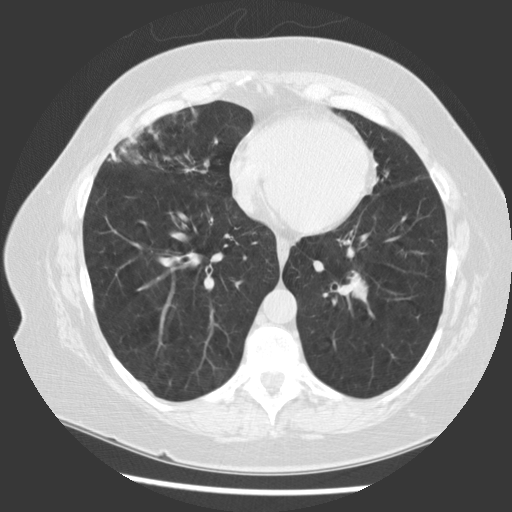
Chest CT (low-dose screening protocol), one axial image, first (baseline) screen, lung window (W 1500 / L -600 HU), 2.5 mm slice thickness, slice 53 of 130 in the series, 512 × 512 image matrix. Female, age 58 years at enrolment. Former smoker at enrolment.
• Expert-annotated lung lesion, bounding box (x1, y1, x2, y2) in pixels: (329, 259, 387, 327).
• Screening reader's record for this exam (one nodule recorded; not confirmed to be the boxed lesion): non-calcified nodule or mass ≥4 mm, left lower lobe, 22 × 15 mm, smooth margins, soft tissue attenuation.
• Later outcome: lung cancer diagnosed 108 days after this screen — carcinoma, NOS, left hilum, stage IA (AJCC 6th edition), 28 mm at pathology.